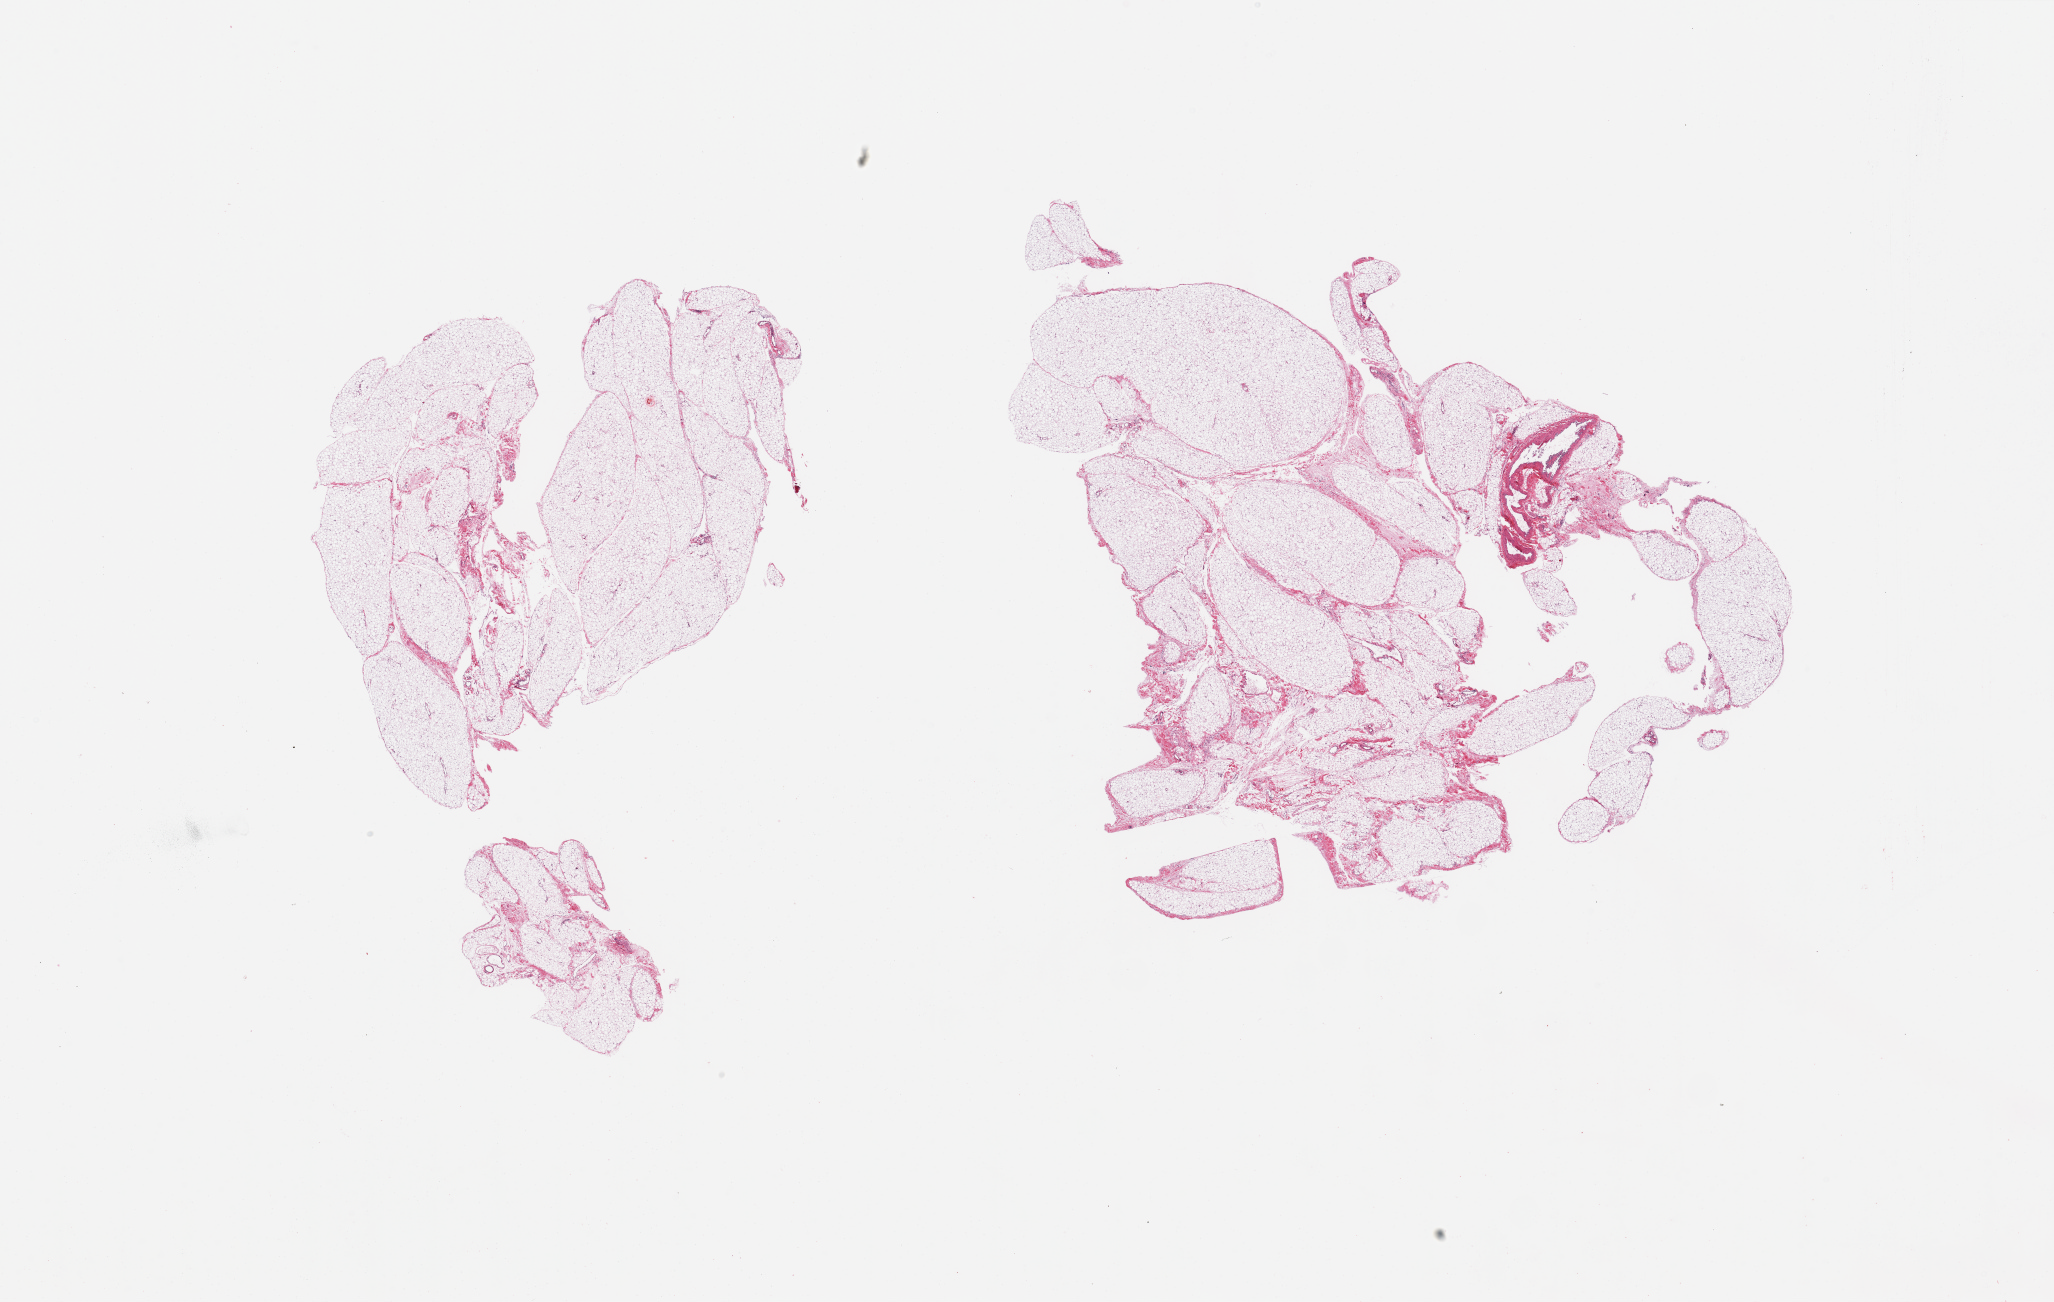
Whole-slide image, H&E stain — low-resolution overview of the scanned area, about 32.5 x 20.6 mm. PAXgene-fixed, paraffin-embedded tissue. Target tissue: omentum. Tissue donor sample. Donor: female.
Review note (as recorded): 2 pieces; mature fat, focal margination of neutrophils.